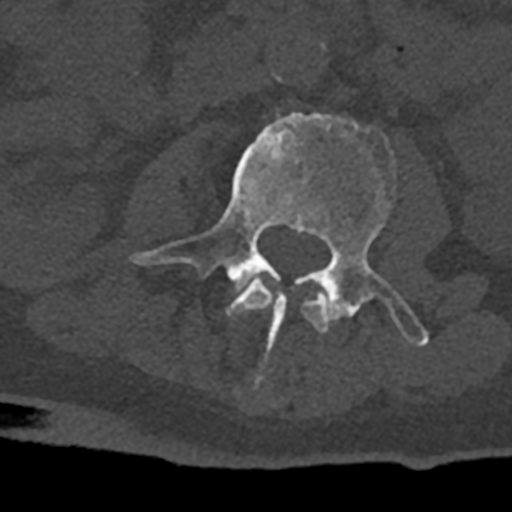
CT including the spine, one axial slice. Slice 330 of 797 in the series (ordered by position). Reconstruction kernel Br40s/3. 120 kVp. Bone window (W 1800 / L 400 HU). 0.5 mm slice thickness. 512 × 512 image matrix, field of view 160 × 160 mm. Male patient, age 74 years. Case-level facts recorded for this patient, not image findings: primary cancer: renal; vertebrae with lytic lesions (as recorded): T10, L1, L2, L3, L4, L5.
Structures marked on this image (semi-automatic segmentation, software-assisted and operator-edited):
- L2 vertebra: bounding box (x1, y1, x2, y2) in pixels: (226, 279, 329, 333)
- L3 vertebra: (128, 112, 429, 349)